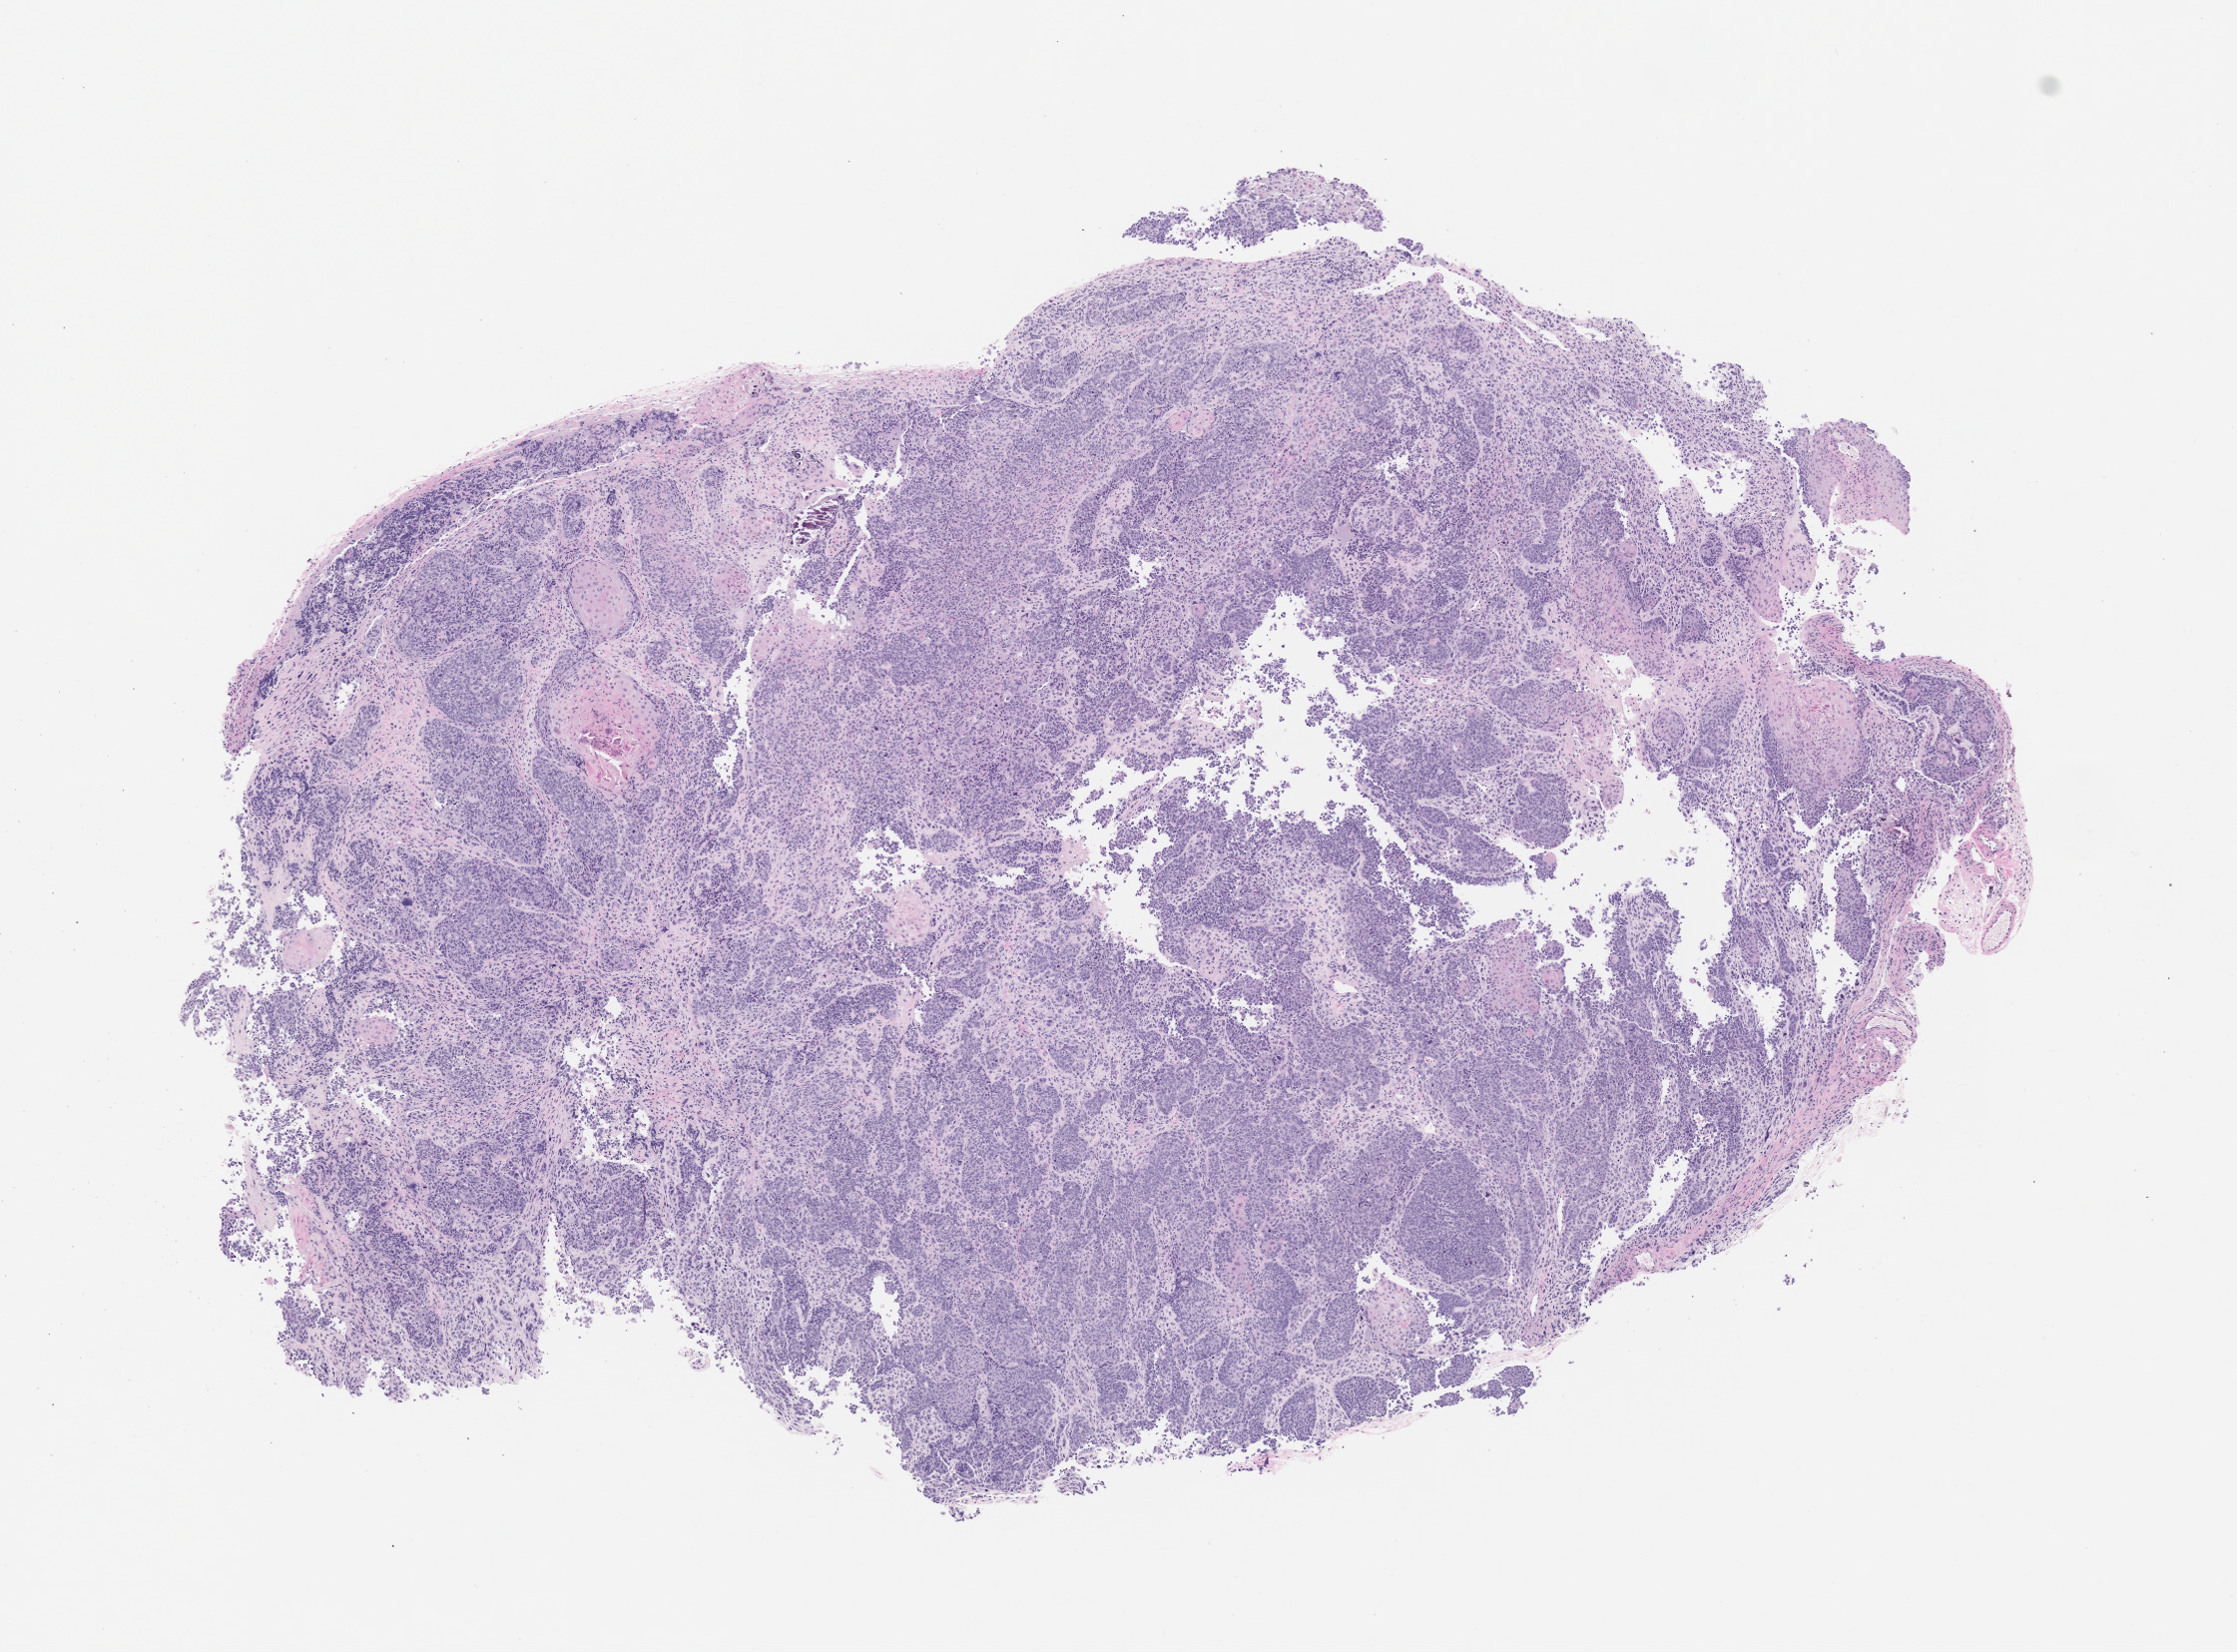
H&E whole-slide image of a patient-derived xenograft (PDX) tumor grown in a mouse, passage 1, low-resolution overview of the scanned area, about 9.0 x 6.7 mm; formalin-fixed, paraffin-embedded (FFPE) tissue; originating tumor site category: female genital tract.
Originating patient diagnosis: Carcinosarcoma.